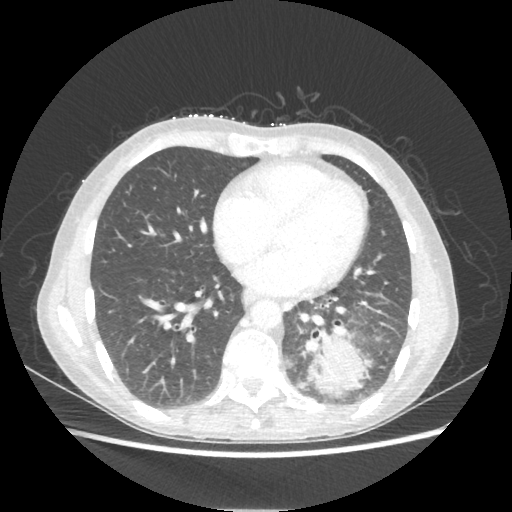
Chest CT, one axial slice. Position 88 of 221 along the scan axis. Reconstruction kernel STANDARD. 80 kVp. Lung window (W 1500 / L -600 HU). 1.25 mm slice thickness. 512 × 512 image matrix. Female patient, age 53 years. Case-level facts recorded for this patient, not image findings: clinical TNM (as recorded): T3 N0 M0.
Annotated regions visible in this slice (bounding box drawn by a radiologist):
- lung tumour (recorded histology: adenocarcinoma): bounding box <299,328,371,398> (left, top, right, bottom; pixels)